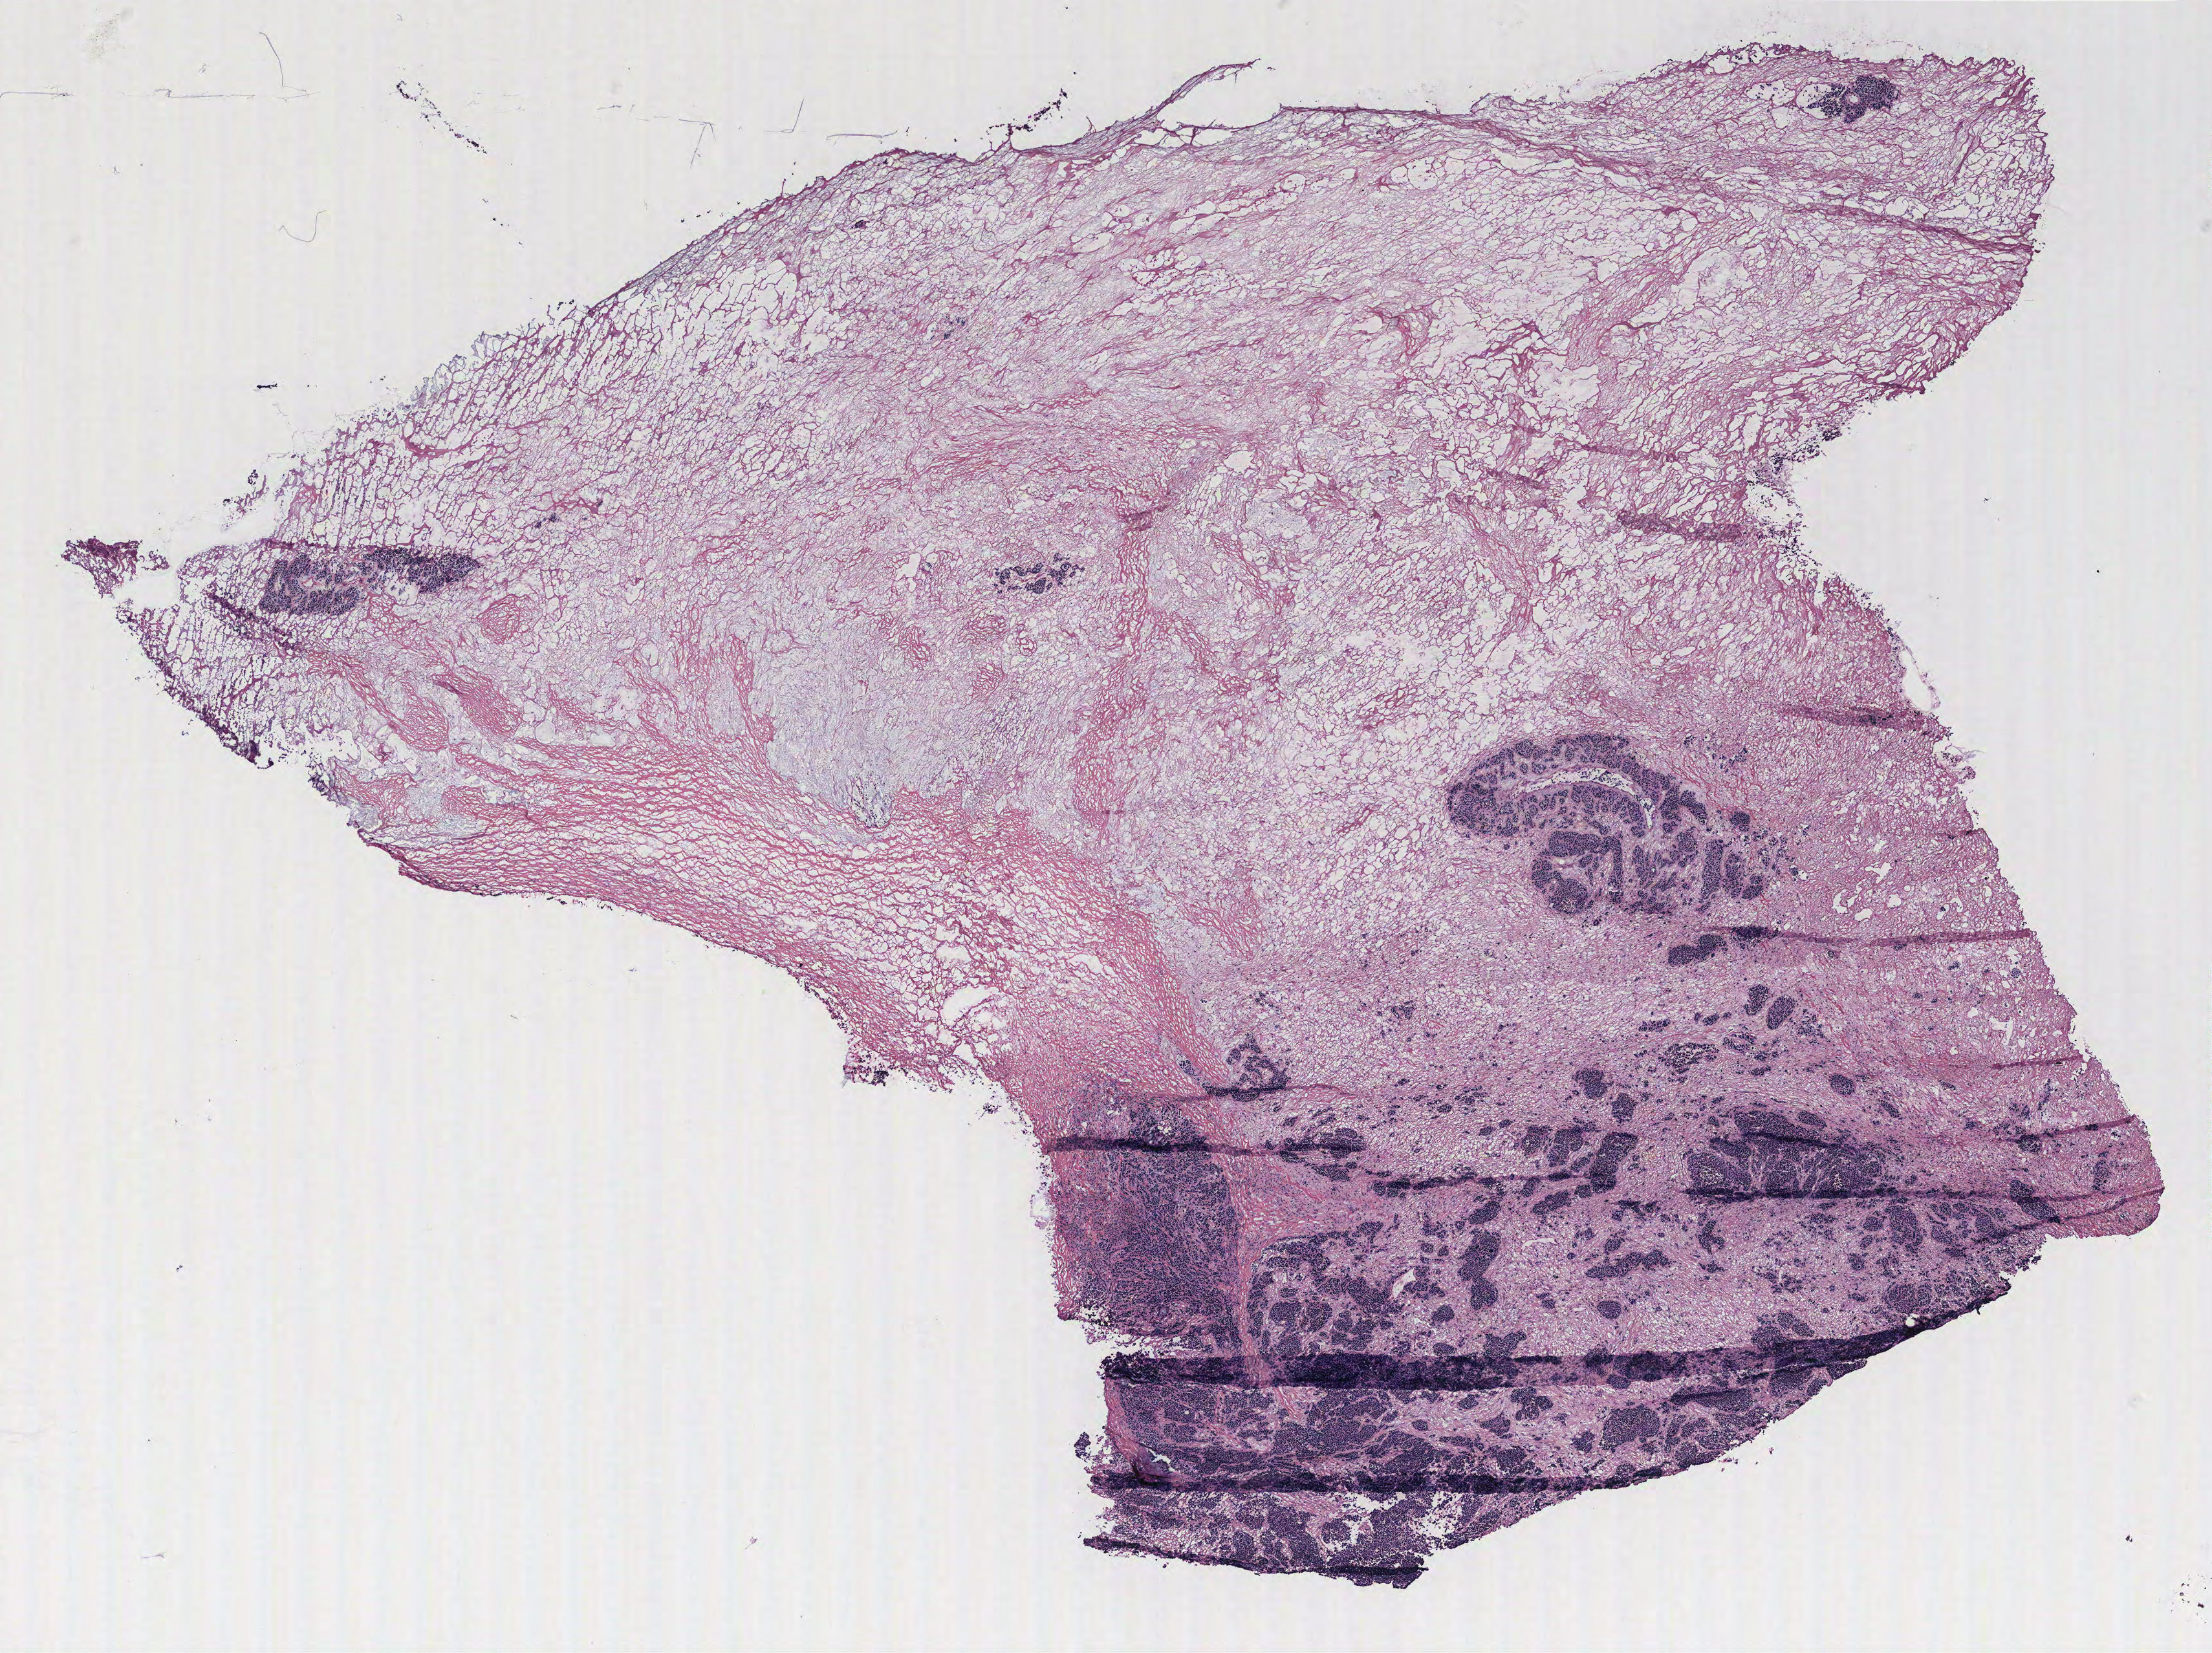
Whole-slide histology image, H&E, a low-resolution overview of the entire scanned area, about 13.7 x 10.2 mm (slide scanned at 40x); ovary, tumour tissue. Female, 57 y/o.
Histologic diagnosis: Serous adenocarcinoma, NOS.